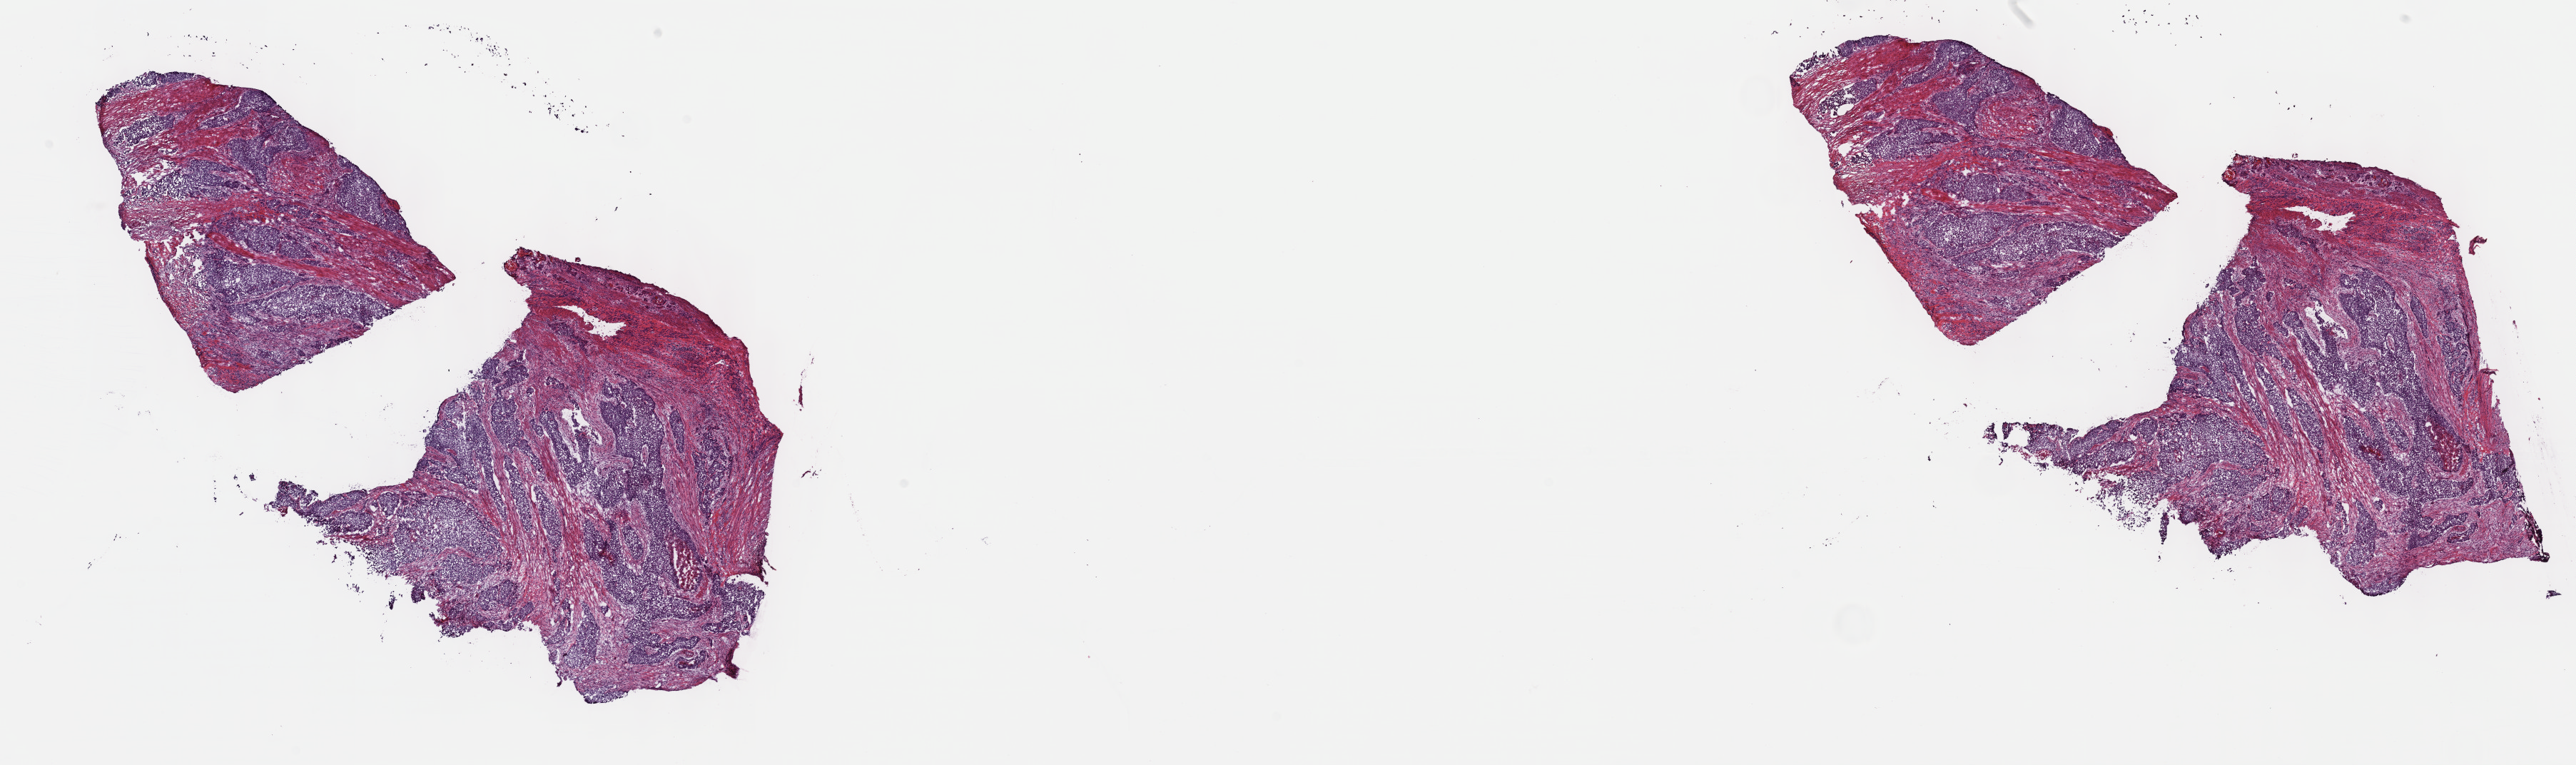
Whole-slide histology image, H&E-stained, low-resolution overview of the scanned area, about 29.2 x 8.7 mm (from a 40x scan); frozen section from the top of the tissue portion; primary tumour sample from the bladder. Patient: male, age at initial diagnosis 86 years. Histologic grade: high grade. Composition of this section per pathologist review: tumour cells 75%, tumour nuclei 75%, normal cells 0%, stromal cells 23%, necrosis 2%. Inflammatory infiltration, as recorded: lymphocyte infiltration 2%, monocyte infiltration 1%, neutrophil infiltration 5%.
Pathologic diagnosis: Transitional cell carcinoma. AJCC pathologic stage: IV (7th edition).